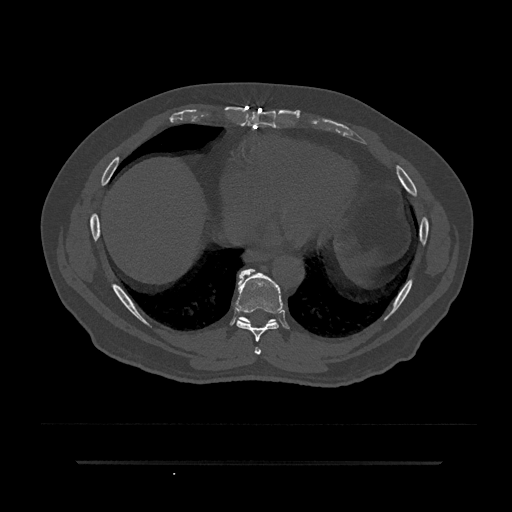
CT including the spine, one axial slice; slice 414 of 797 in the series (ordered by position); reconstruction kernel Br40s/3; 120 kVp; bone window (W 1800 / L 400 HU); 512 × 512 image matrix, field of view 464 × 464 mm. Male patient, age 59 years. Case-level facts recorded for this patient, not image findings: primary cancer: bile ducts.
Outlined on this slice (semi-automatic segmentation, software-assisted and operator-edited):
- T7 vertebra: bounding box <254,347,261,355> (left, top, right, bottom; pixels)
- T8 vertebra: <235,269,283,355>
- T9 vertebra: <238,273,276,323>